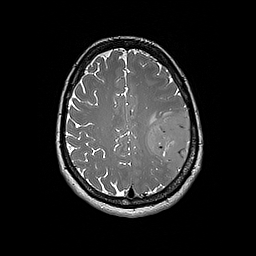
Brain MRI from a brain-tumour surgery series, one axial slice; position 69 of 192 along the scan axis; 1 mm slice thickness; 256 × 256 image matrix, field of view 250 × 250 mm. From the clinical record (not read from this slice): histopathology: Glioblastoma; WHO grade: 4.
Structures marked on this image (expert manual segmentation):
- tumour: bounding box (x1, y1, x2, y2) in pixels: (147, 114, 191, 167)